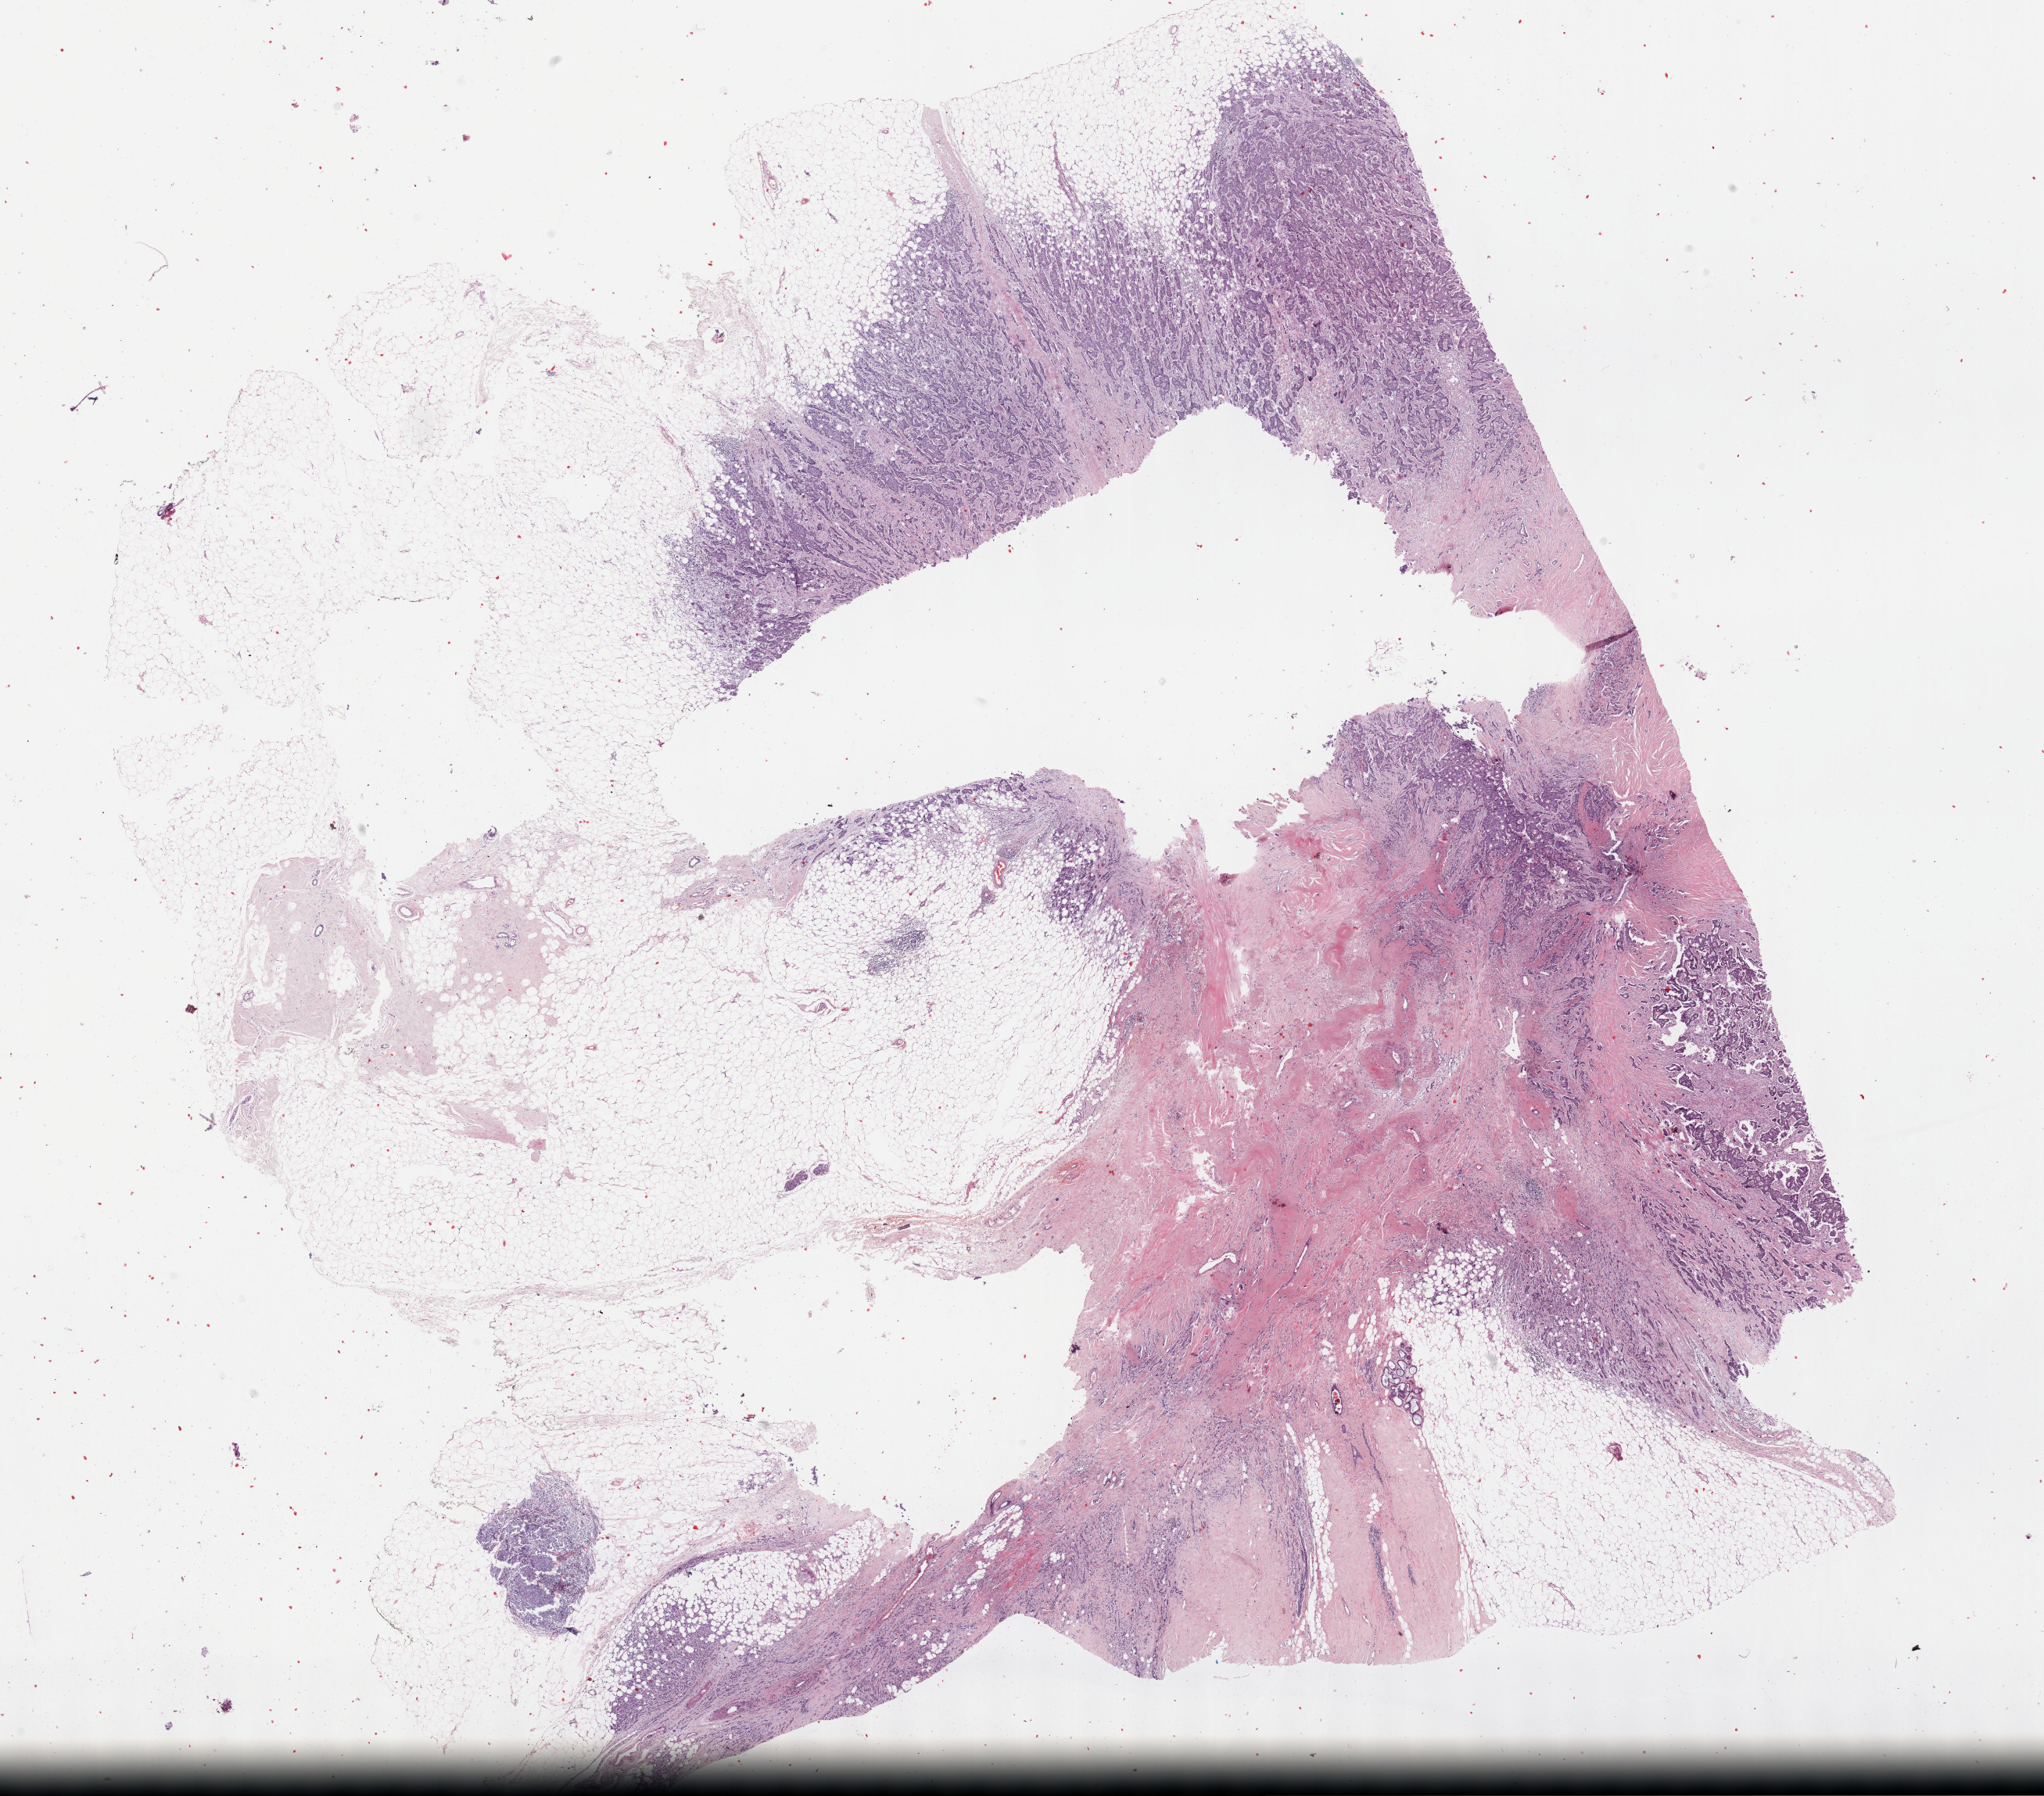
Whole-slide histology image, Hematoxylin and eosin (H&E) stained, shown as a low-resolution overview of the whole scanned area (about 21.1 x 18.6 mm), FFPE section, breast, primary tumour sample. Female, age 62 years at initial diagnosis.
• AJCC pathologic stage: IIA (7th edition)
• pathologic diagnosis: Infiltrating duct carcinoma, NOS